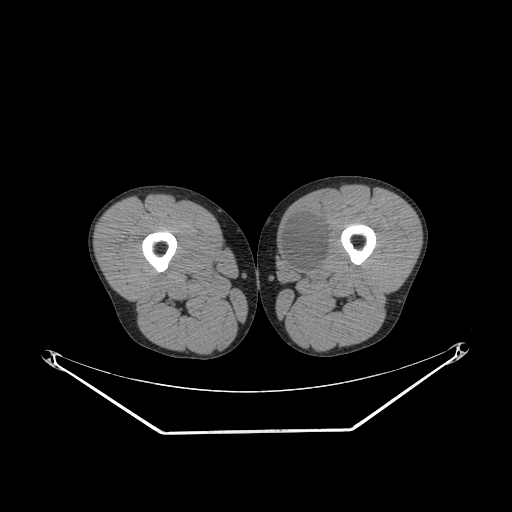
CT of an extremity soft-tissue mass (from a PET/CT study), one axial slice. Slice 246 of 311 in the series (ordered by position). Reconstruction kernel SOFT. Soft-tissue window (W 400 / L 40 HU). 512 × 512 image matrix. Male patient. Case-level facts recorded for this patient, not image findings: histological type: mixoid liposarcoma; grade: low; site of the primary tumour: left thigh.
Outlined on this slice (expert contour drawn on MRI and transferred to this co-registered scan by the dataset authors):
- gross tumour volume (mass): box from (x=281, y=215) to (x=330, y=275) px